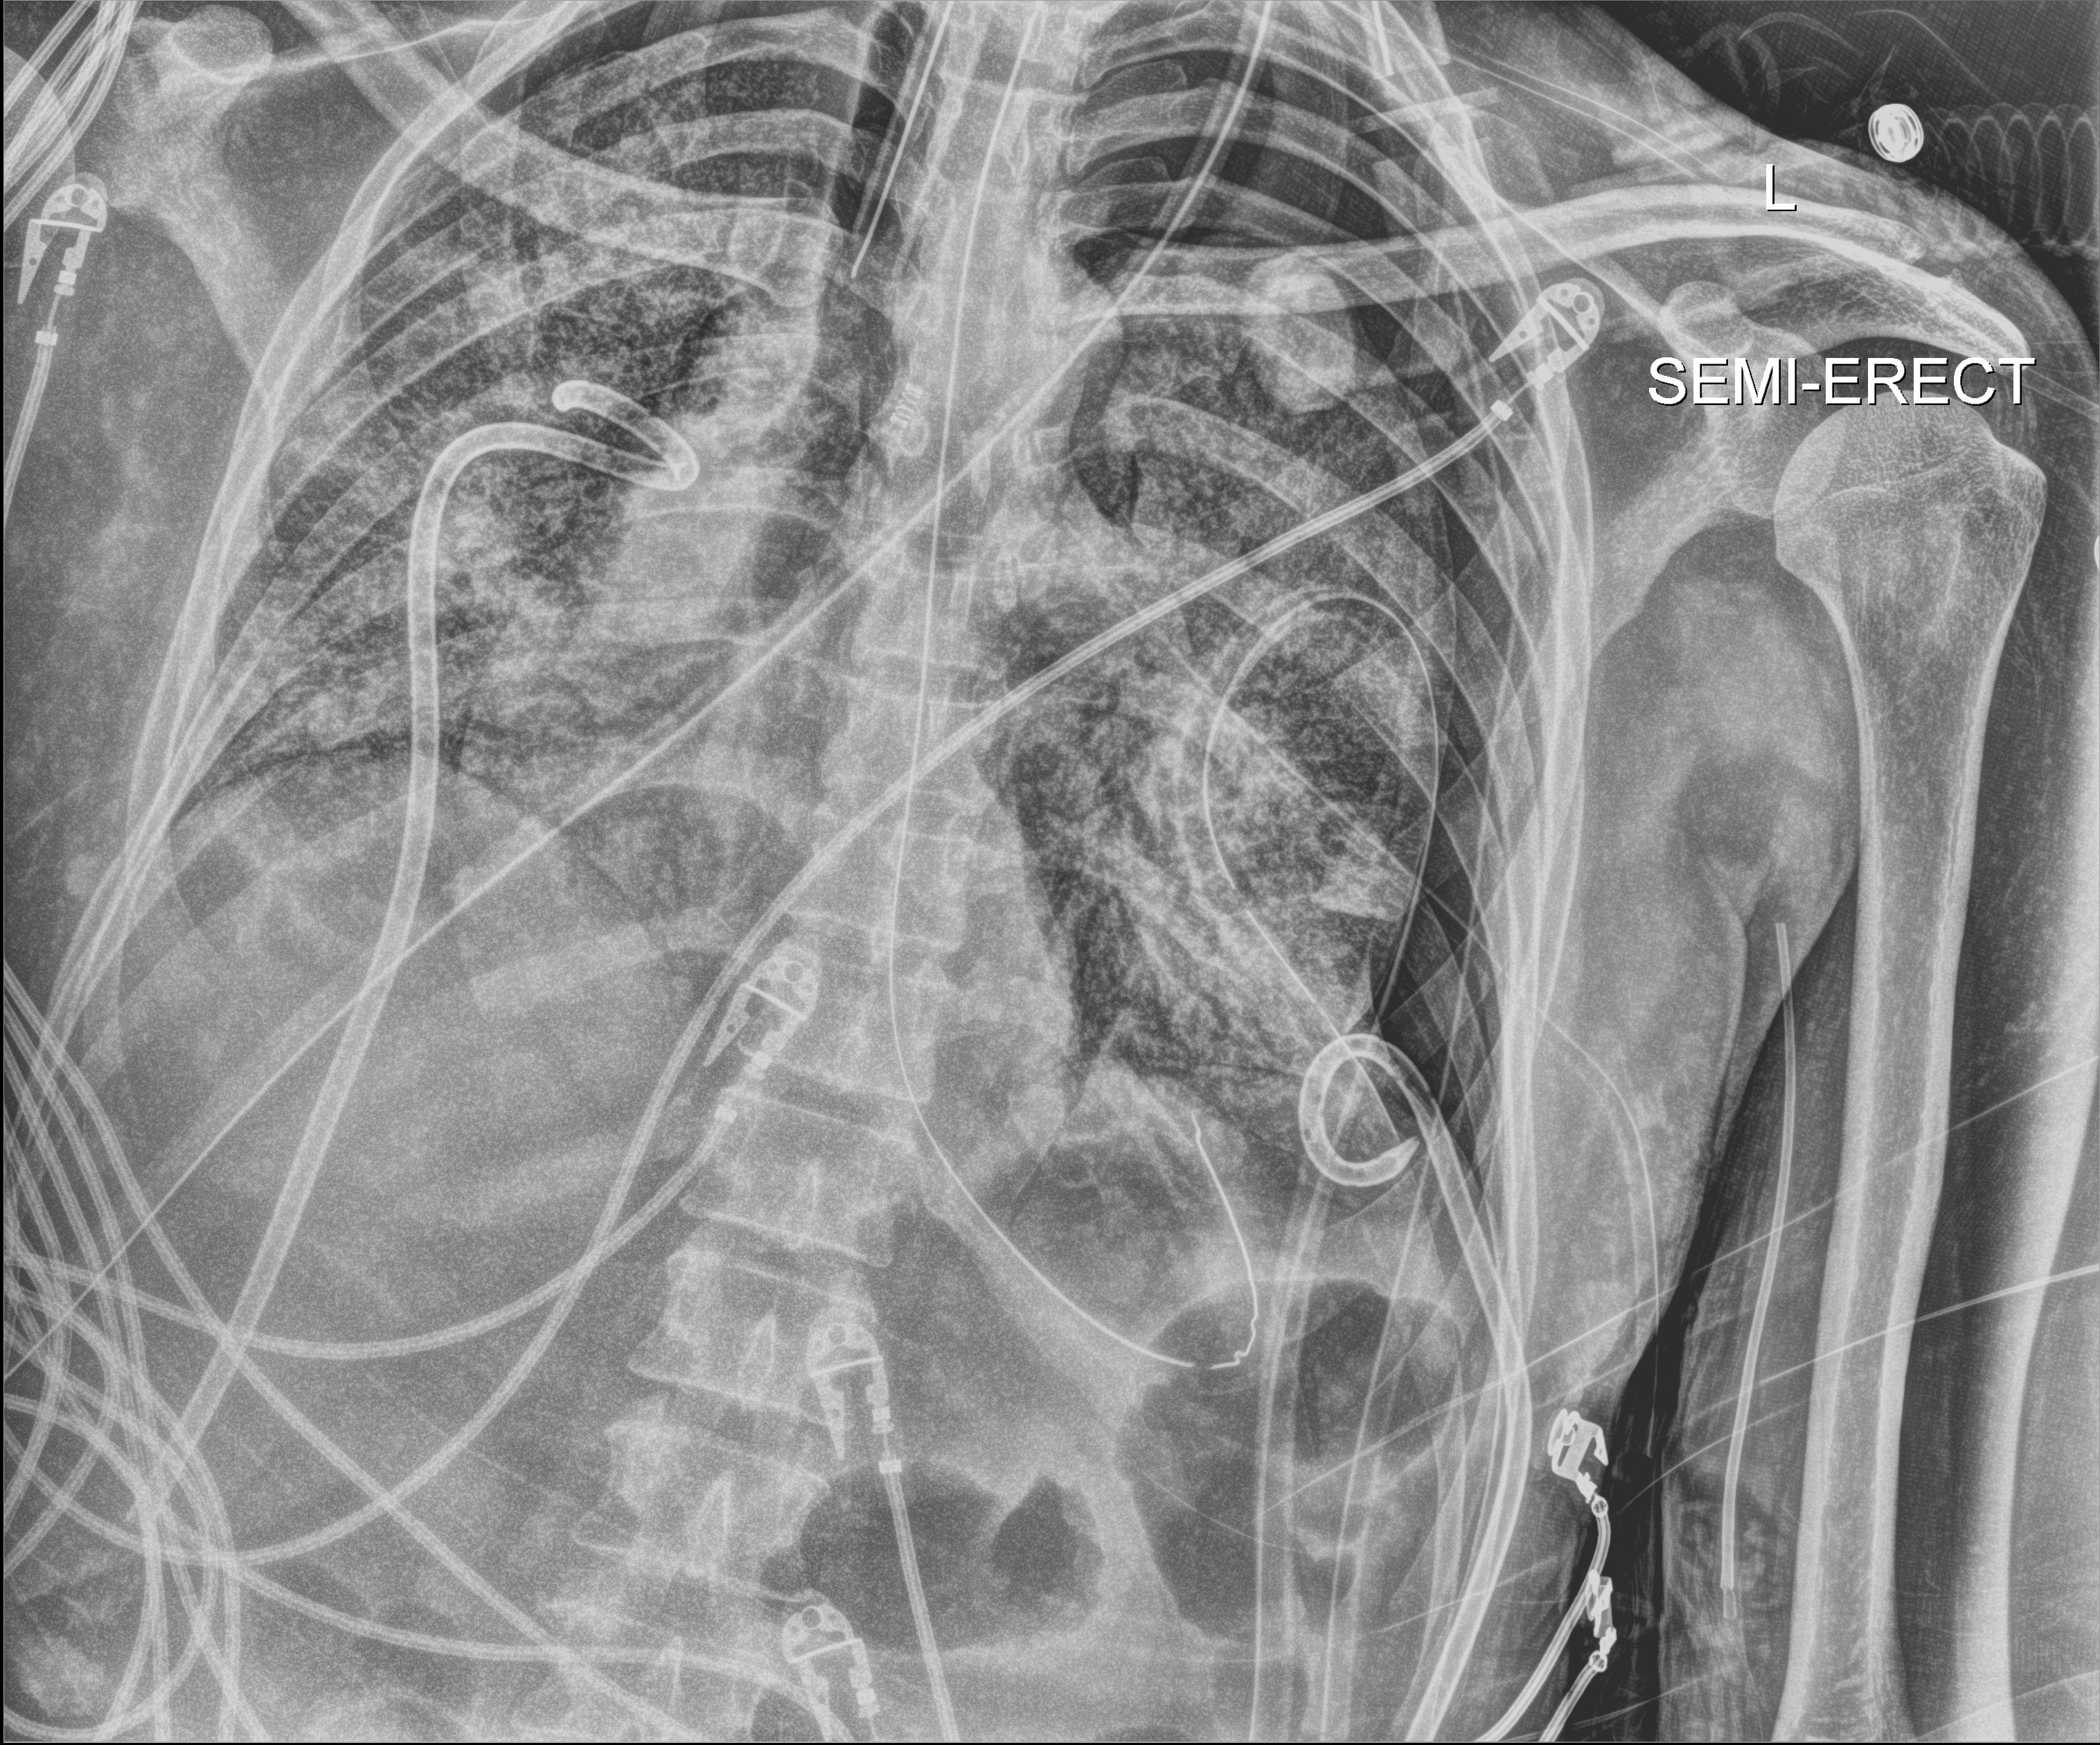
Portable chest radiograph, anteroposterior (AP) projection. Patient hospitalised with COVID-19, aged 18–59 years.
From the hospital-stay record, not from the radiograph (when in the stay this image was taken is not recorded): mechanically ventilated during this hospital stay: yes; admitted to intensive care during this hospital stay: yes; diabetes (admission record): no.